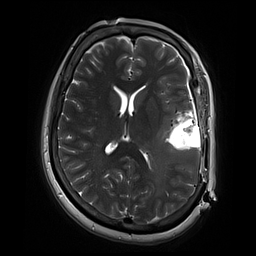
Brain MRI from a brain-tumour surgery series, one axial slice; position 34 of 70 along the scan axis; 2 mm slice thickness; 256 × 256 image matrix, field of view 220 × 220 mm. Case-level facts recorded for this patient, not image findings: histopathology: Glioblastoma; WHO grade: 4; IDH mutation: no; tumour location: Left Temporal.
Annotated regions visible in this slice (outlined manually by an expert reader):
- residual tumour: bounding box (x1, y1, x2, y2) in pixels: (156, 116, 172, 140)